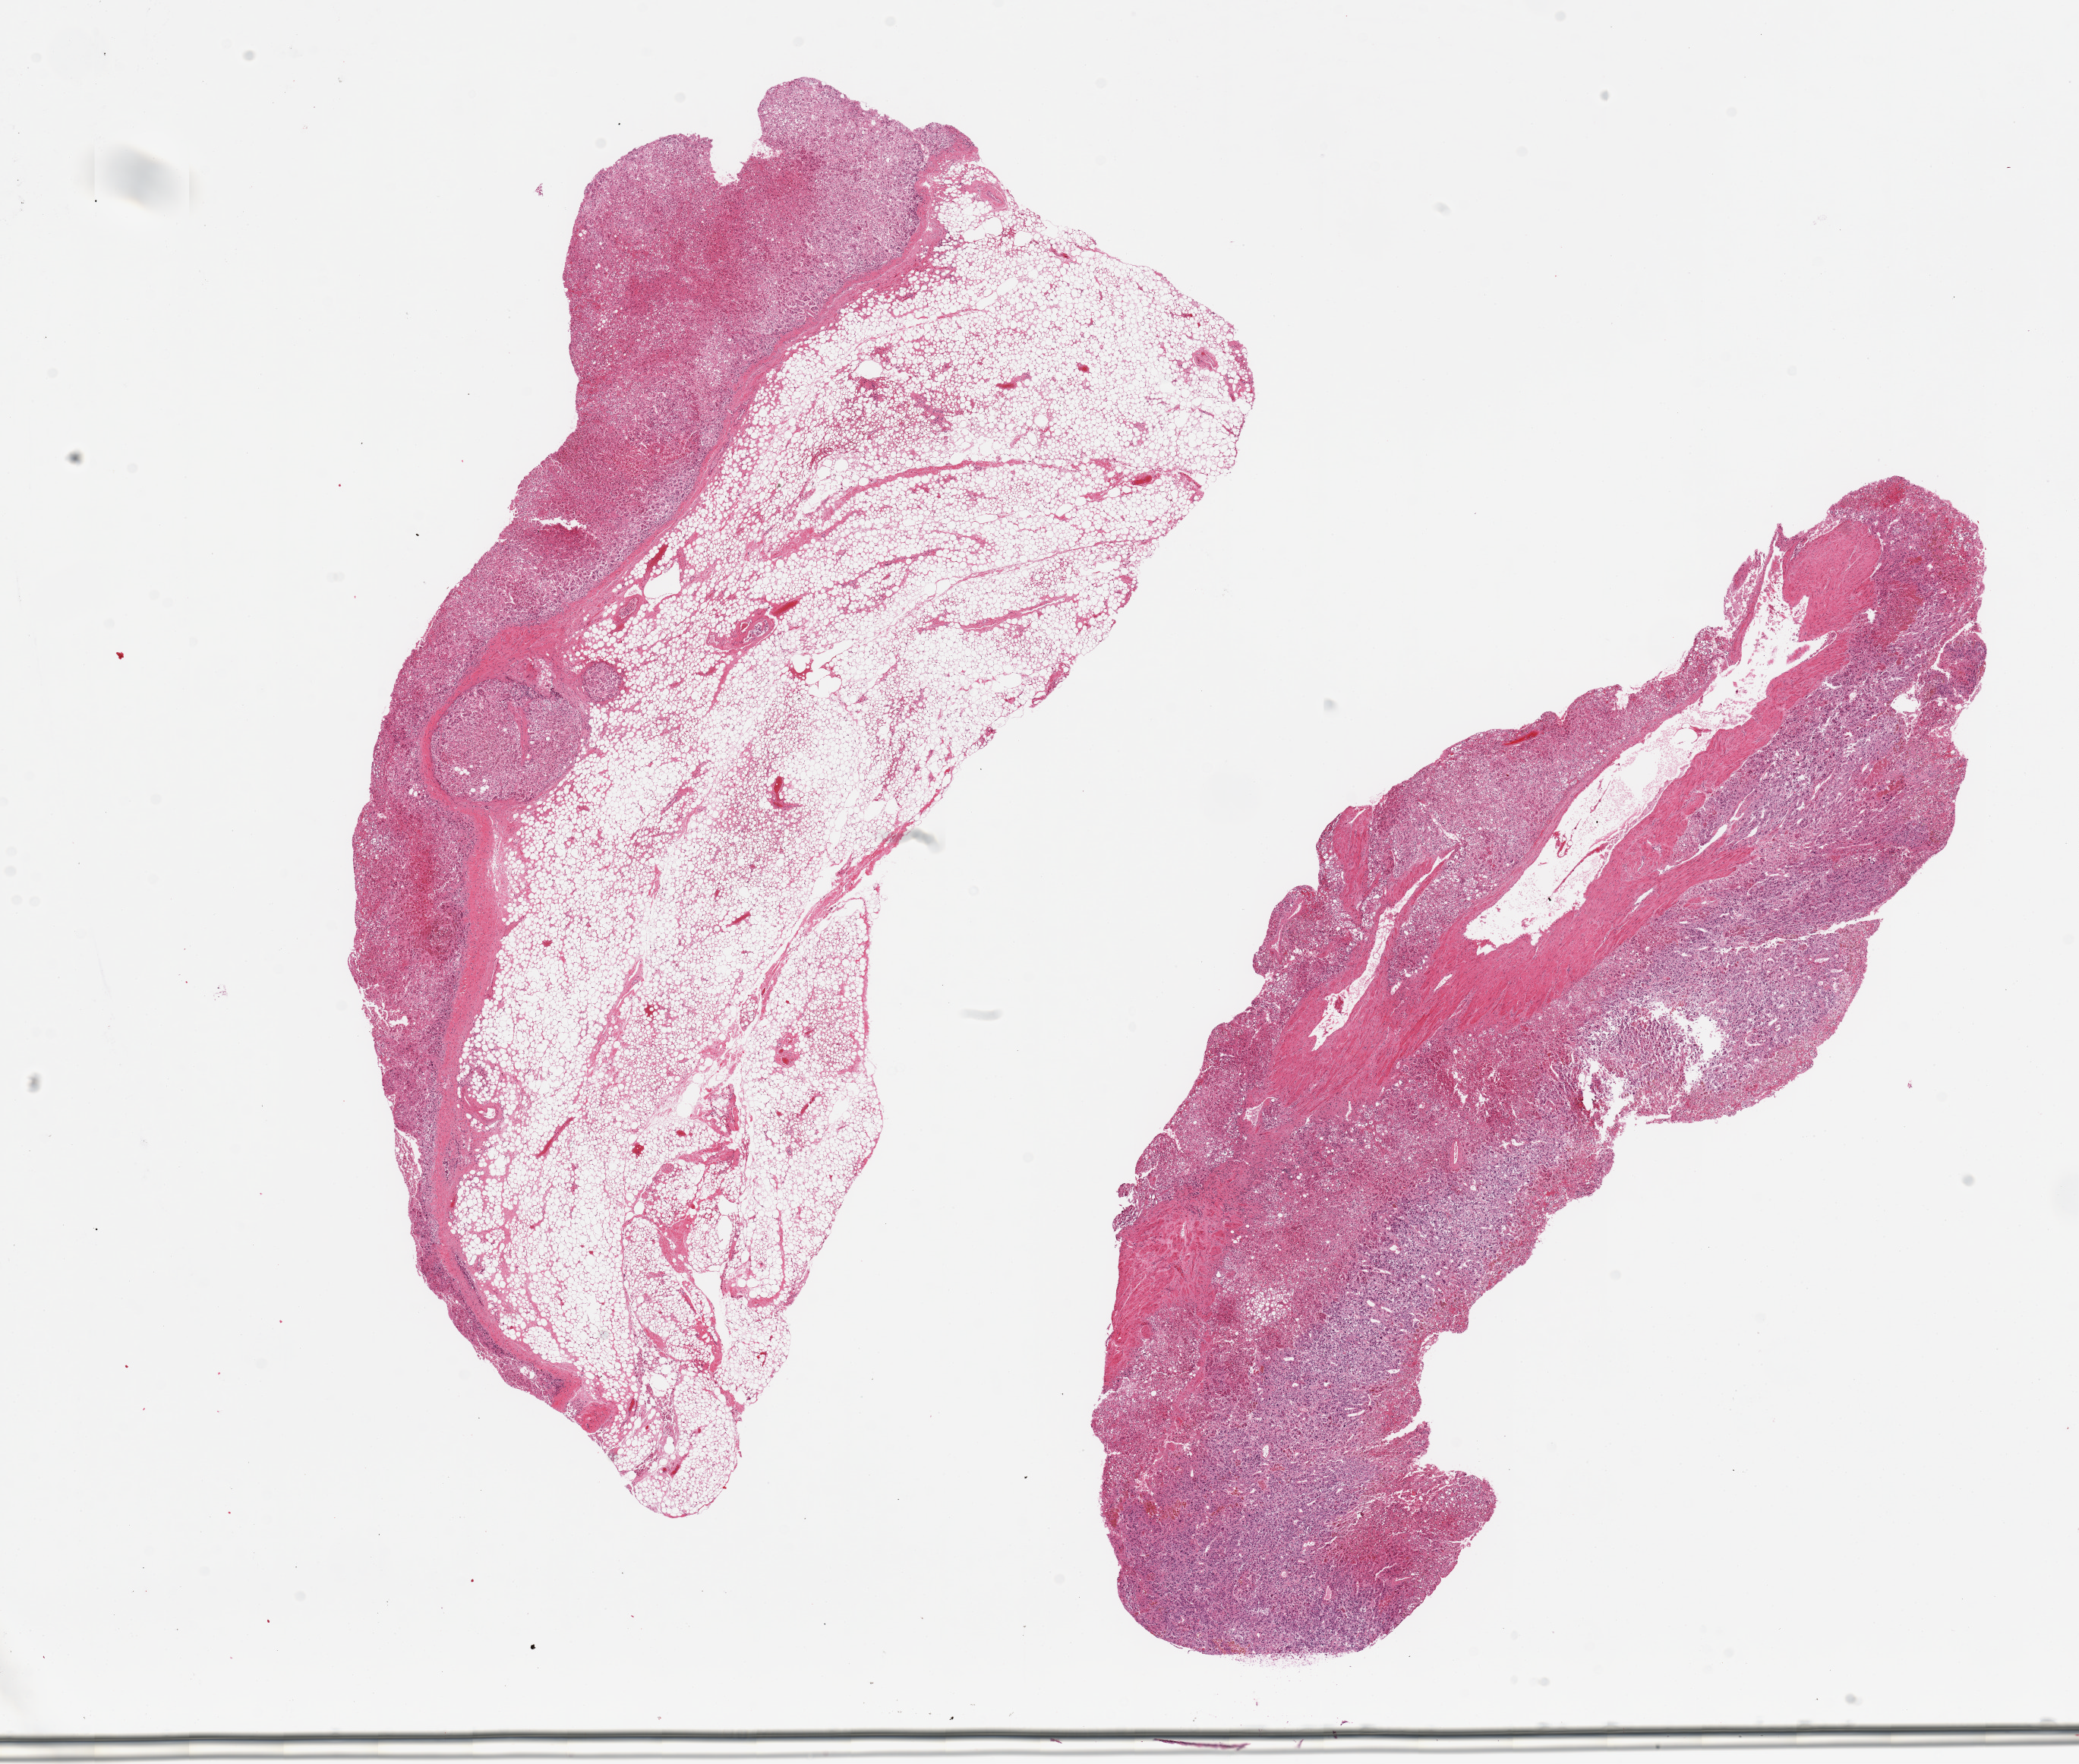
Digitized haematoxylin and eosin-stained section — shown as a low-resolution overview of the whole scanned area (about 21.7 x 18.4 mm, slide scanned at 20x), PAXgene-fixed, paraffin-embedded tissue, section of adrenal gland (target tissue), tissue donor sample. Donor: male.
- reviewer comment on this tissue sample: 2 pieces; 1 with 70% fat, other 10%